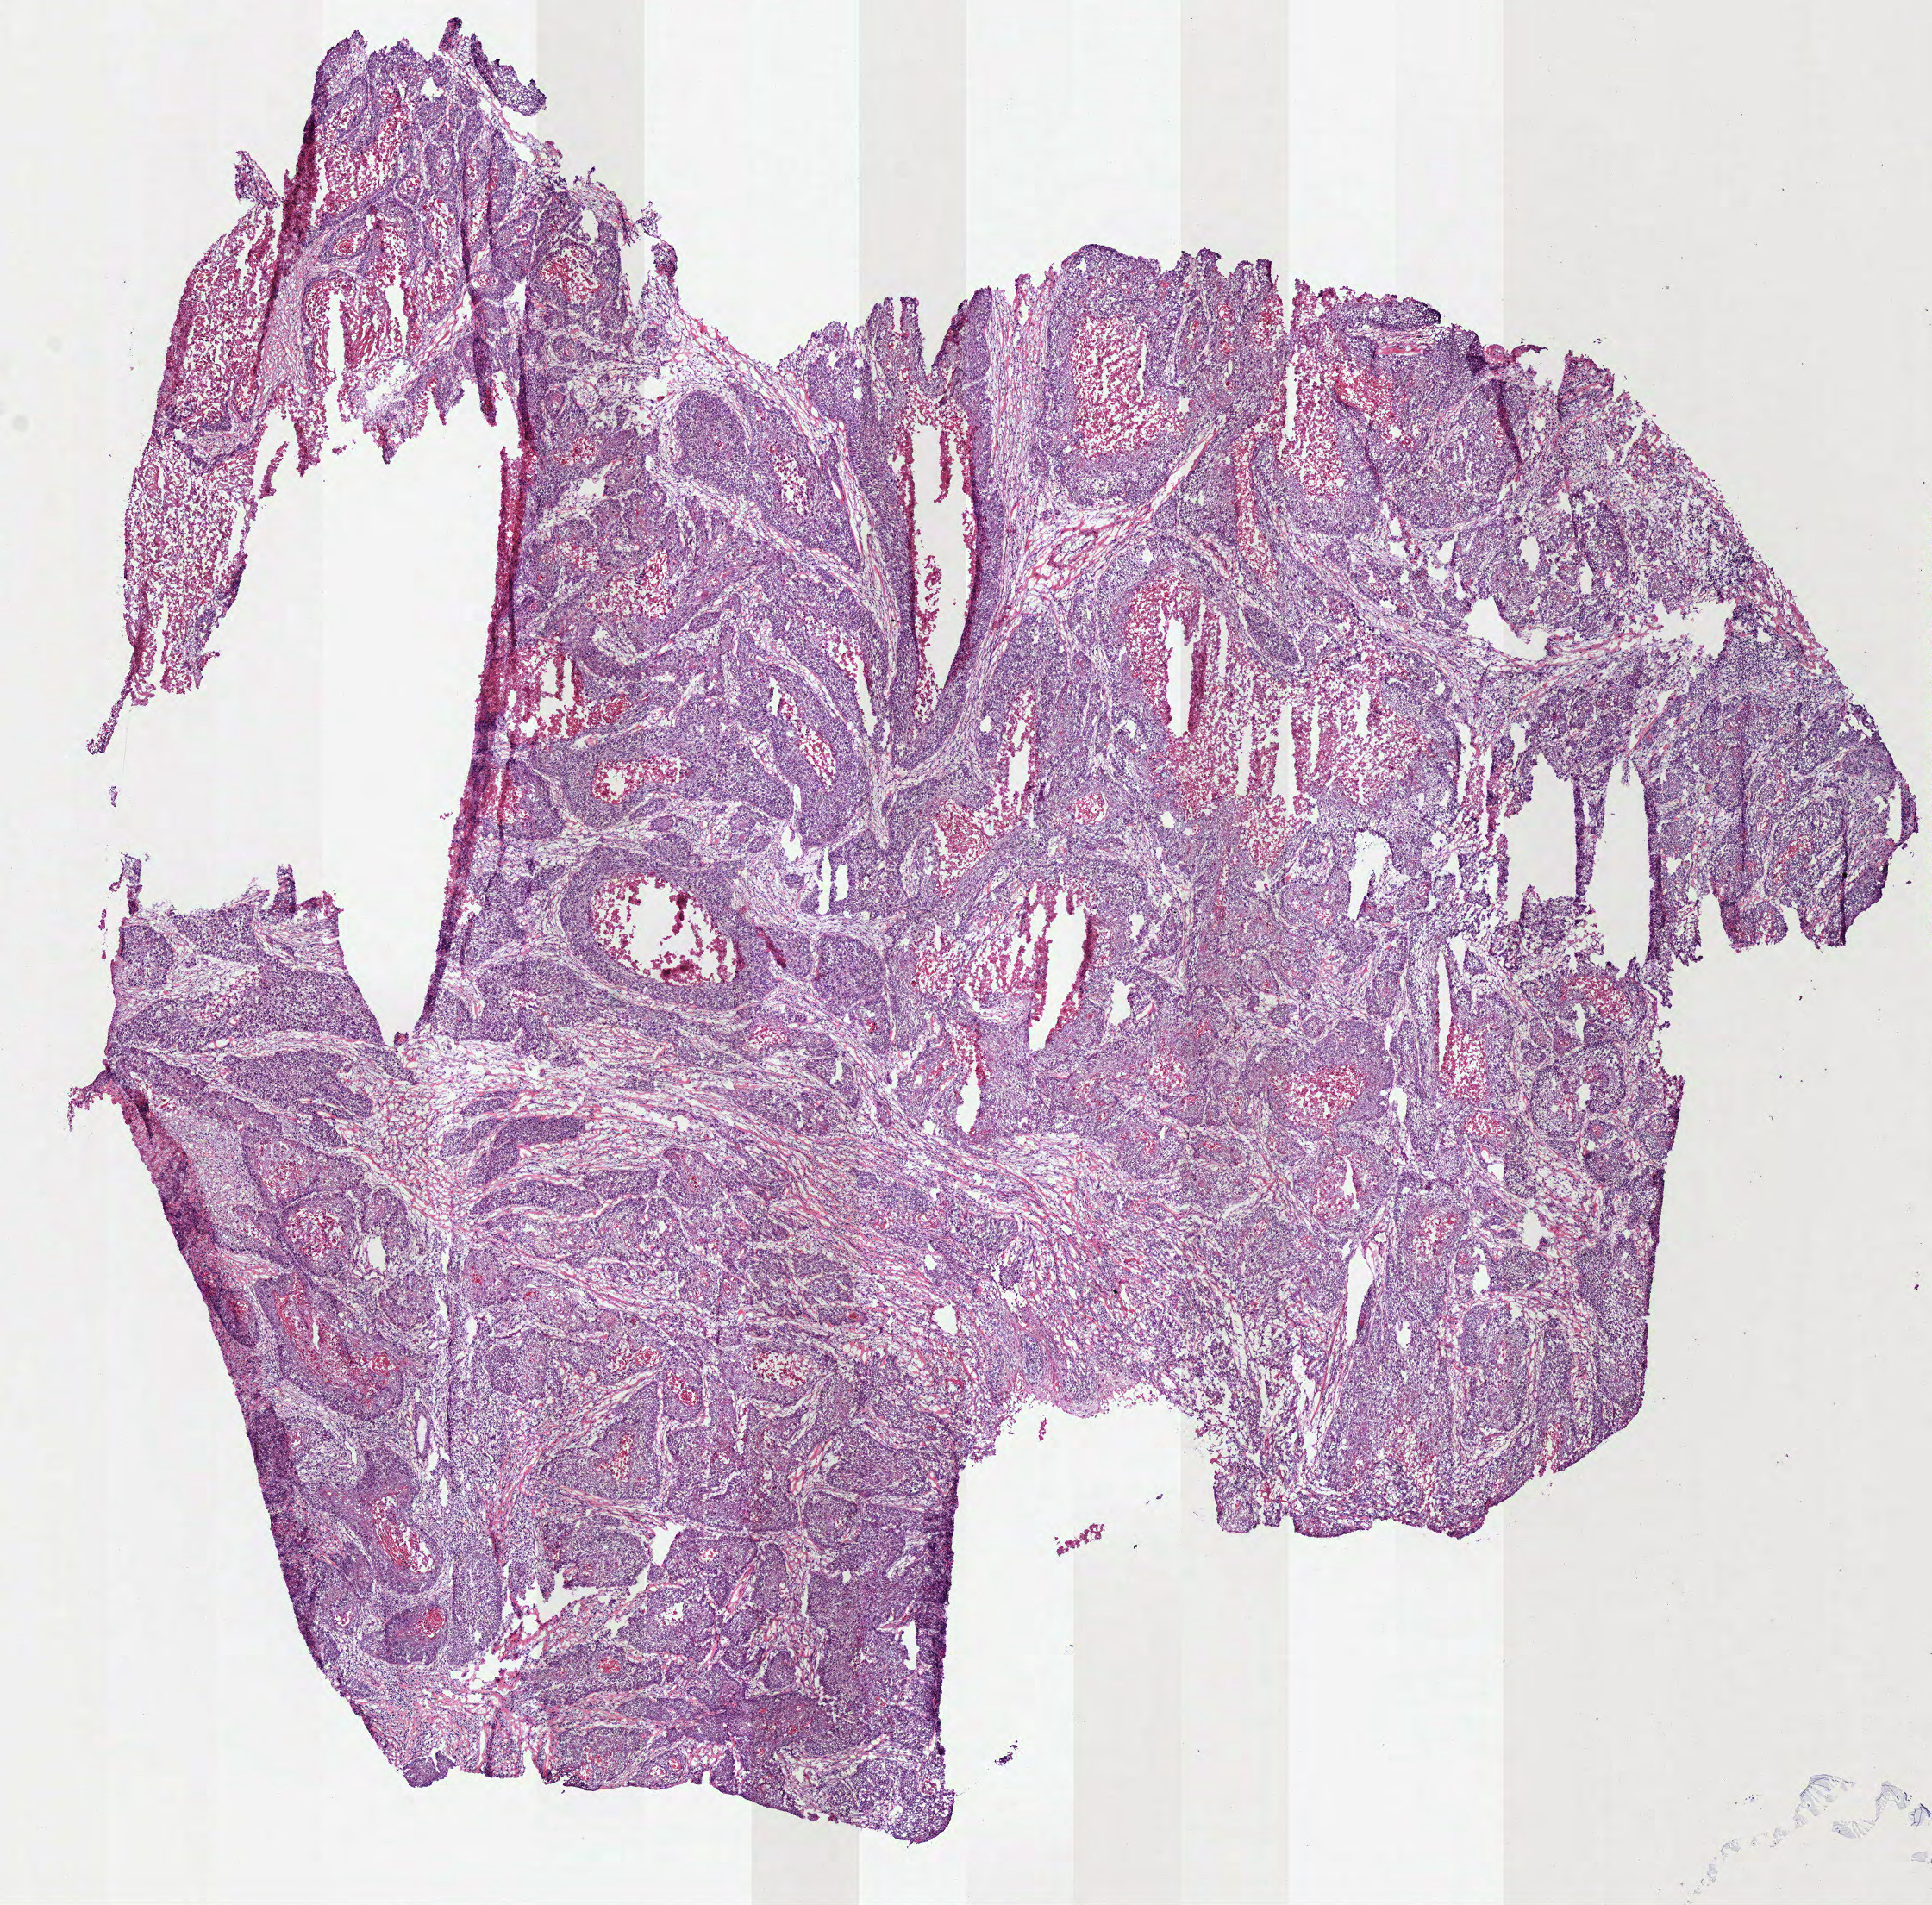
Whole-slide histology image, H&E-stained — whole scanned area (about 8.8 x 8.7 mm) shown as a low-resolution overview; frozen section from the bottom of the tissue portion; primary tumour sample from the head and neck. Male patient; age at initial diagnosis 61 years. Histologic grade: G2 (moderately differentiated). Composition of this section per pathologist review: tumour cells 90%, tumour nuclei 68%, normal cells 0%, stromal cells 10%, necrosis 0%.
AJCC pathologic stage: IVA. Pathologic diagnosis: Squamous cell carcinoma, NOS (larynx, NOS).